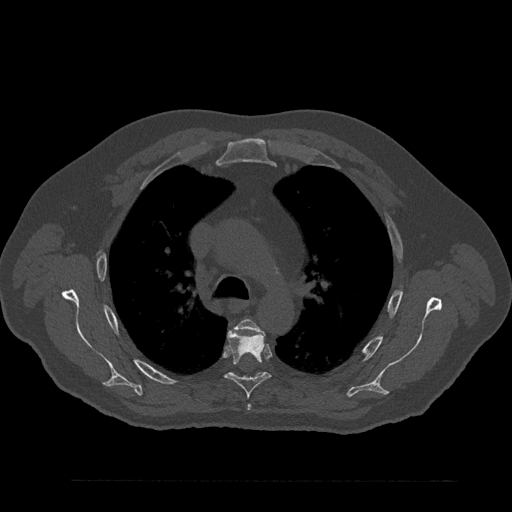
CT including the spine, one axial slice; slice 604 of 797 in the series (ordered by position); 120 kVp; bone window (W 1800 / L 400 HU); 0.5 mm slice thickness; 512 × 512 image matrix, field of view 430 × 430 mm. Patient: male, 61 years. From the clinical record (not read from this slice): primary cancer: prostate.
Annotated regions visible in this slice (semi-automatic segmentation, software-assisted and operator-edited):
- T4 vertebra: box from (x=236, y=319) to (x=259, y=410) px
- T5 vertebra: (x=225, y=330)–(x=271, y=398)
- T6 vertebra: (x=231, y=373)–(x=265, y=378)